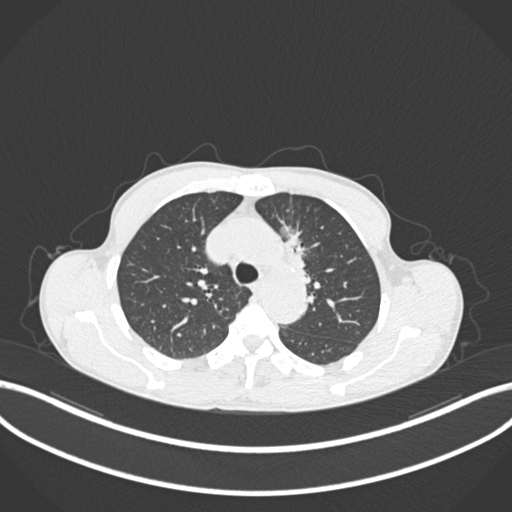
Chest CT, one axial slice; reconstruction kernel B30f; lung window (W 1500 / L -600 HU); 1 mm slice thickness; 512 × 512 image matrix. Male patient, age 58 years. Case-level facts recorded for this patient, not image findings: clinical TNM (as recorded): T1c N1 M0.
Structures marked on this image (rectangle marked by the reading radiologist):
- lung tumour (recorded histology: adenocarcinoma): bounding box <275,212,314,280> (left, top, right, bottom; pixels)